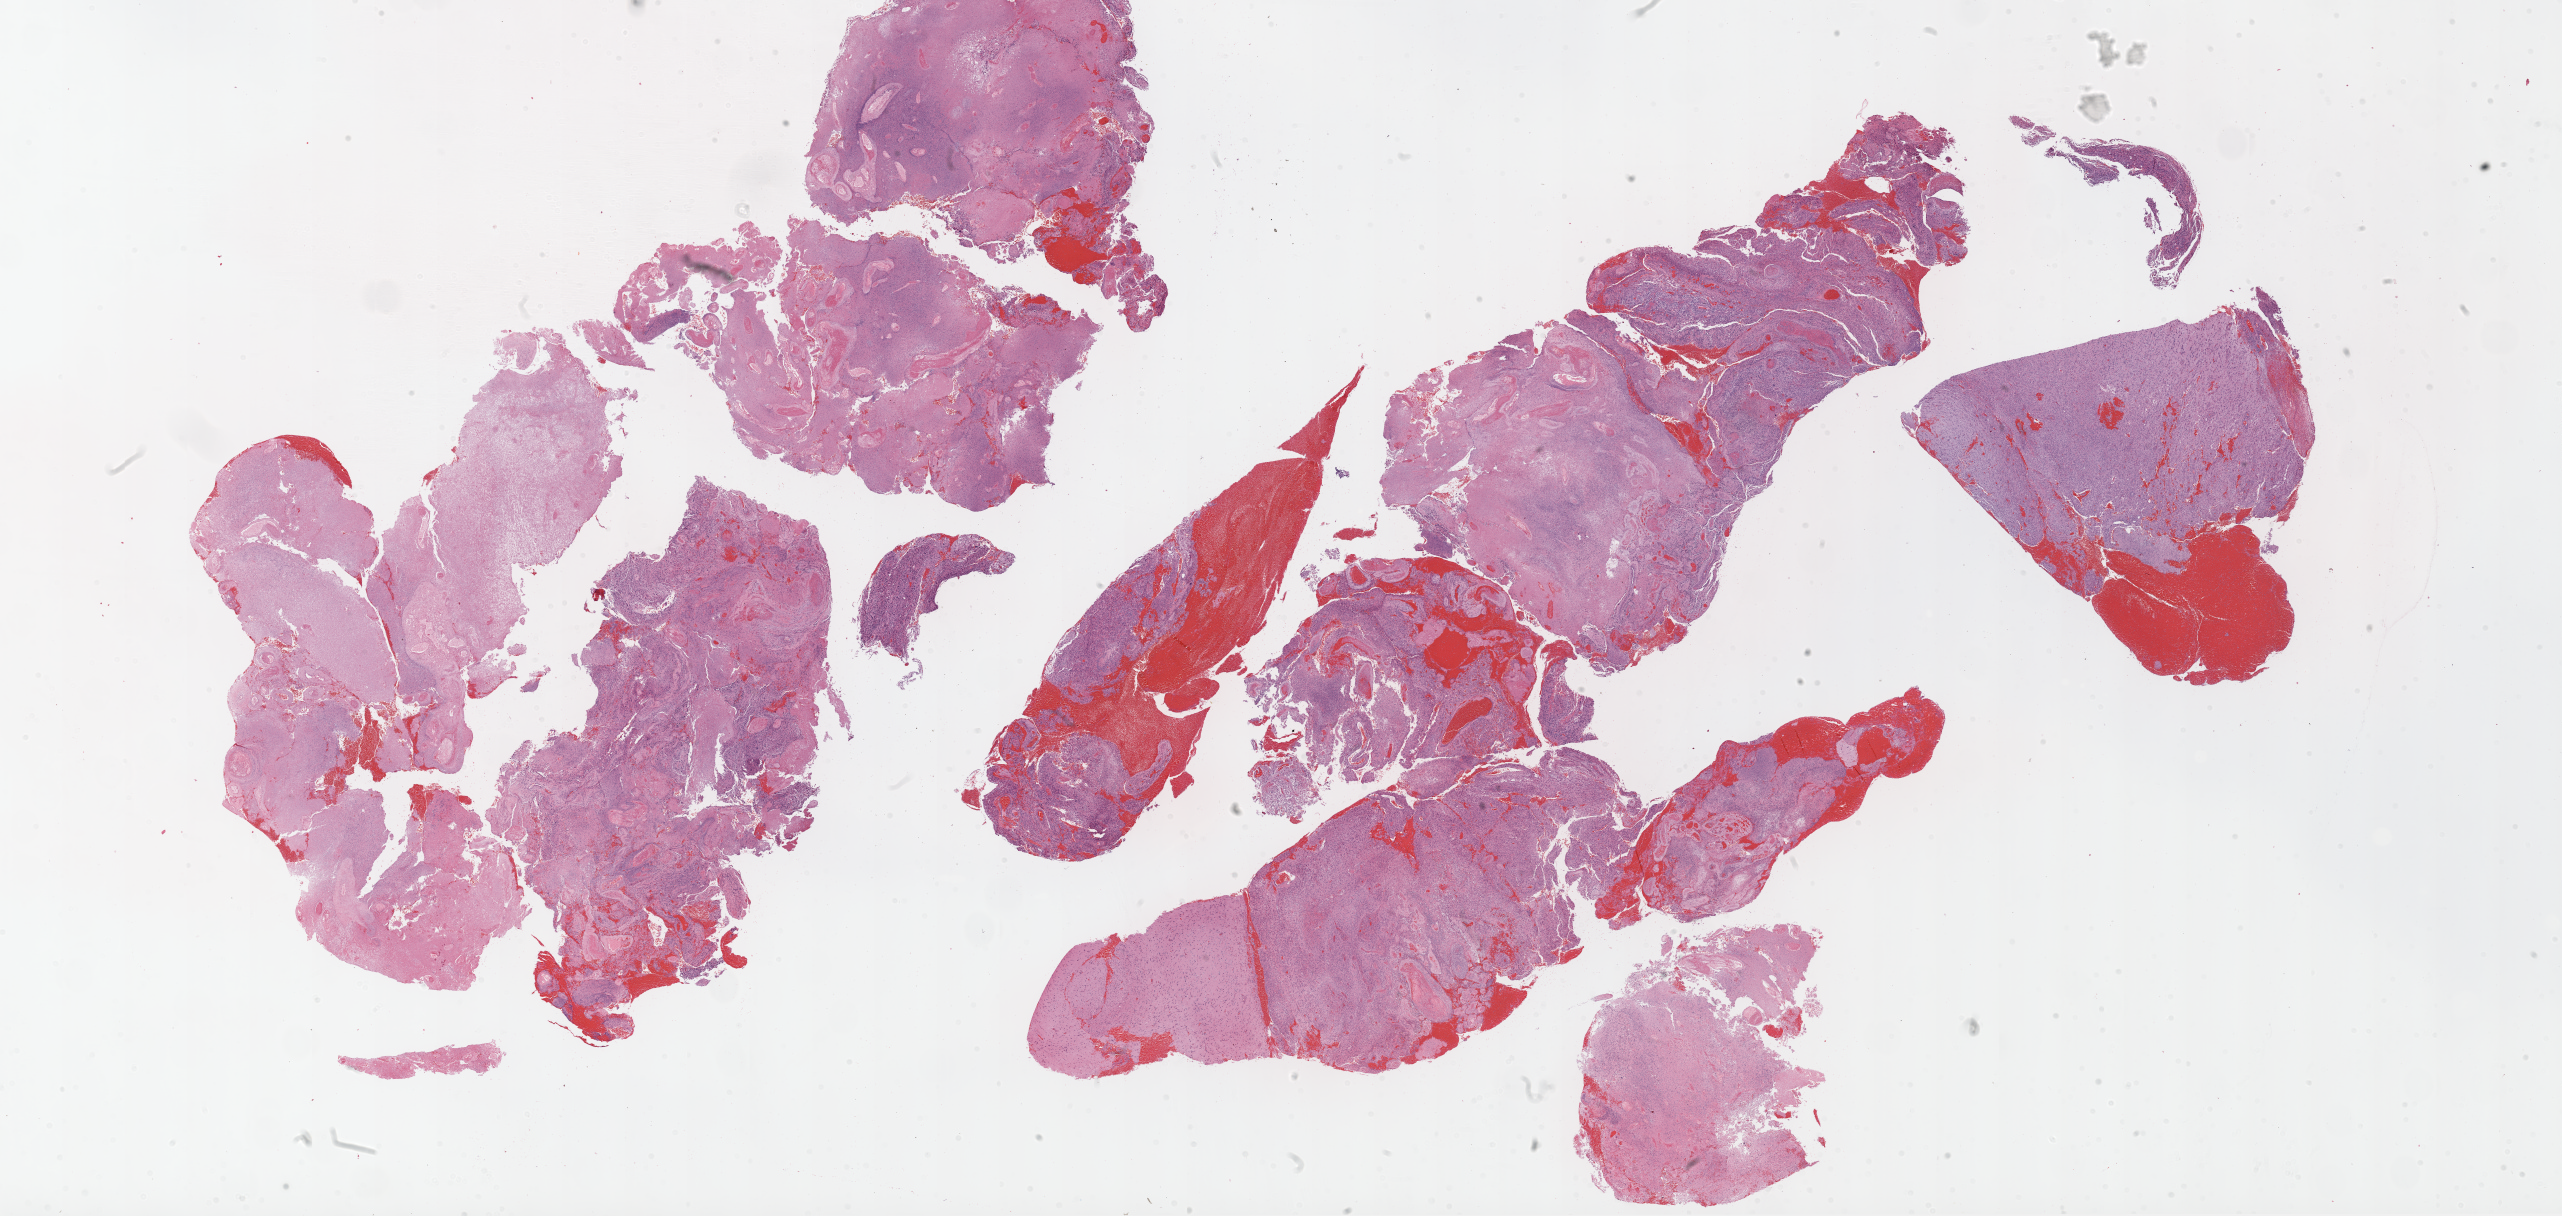
Hematoxylin and eosin (H&E) stained whole-slide image, shown as a low-resolution overview of the whole scanned area (about 41.1 x 19.5 mm, from a 20x scan). Formalin-fixed paraffin-embedded (FFPE) diagnostic section. Brain, primary tumour sample. Patient: male, age at initial diagnosis 55 years.
Pathologic diagnosis: Glioblastoma.